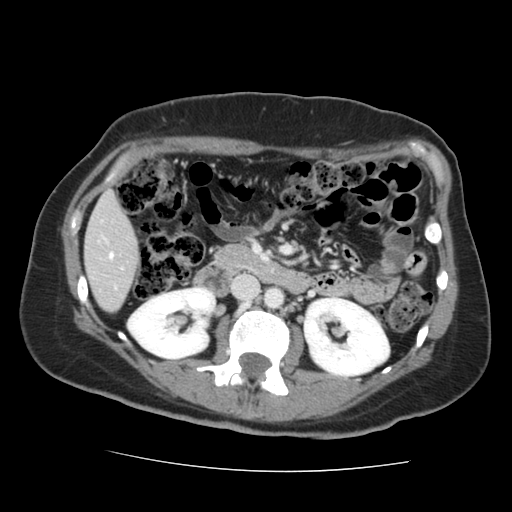
Contrast-enhanced abdominal CT, one axial slice. Position 58 of 144 along the scan axis. Intravenous contrast given. Soft-tissue window (W 400 / L 40 HU). 512 × 512 image matrix, field of view 333 × 333 mm. Female patient, age 46 years. From the clinical record (not read from this slice): diagnosis: colorectal cancer liver metastases, imaged before liver resection; multiple liver metastases: no; largest metastasis: 2.8 cm.
Outlined on this slice (expert manual segmentation):
- liver: box from (x=85, y=195) to (x=137, y=311) px
- planned liver remnant (the part of the liver to remain after resection): (x=85, y=195)–(x=136, y=253)
- portal vein (with intrahepatic branches): (x=109, y=254)–(x=113, y=259)